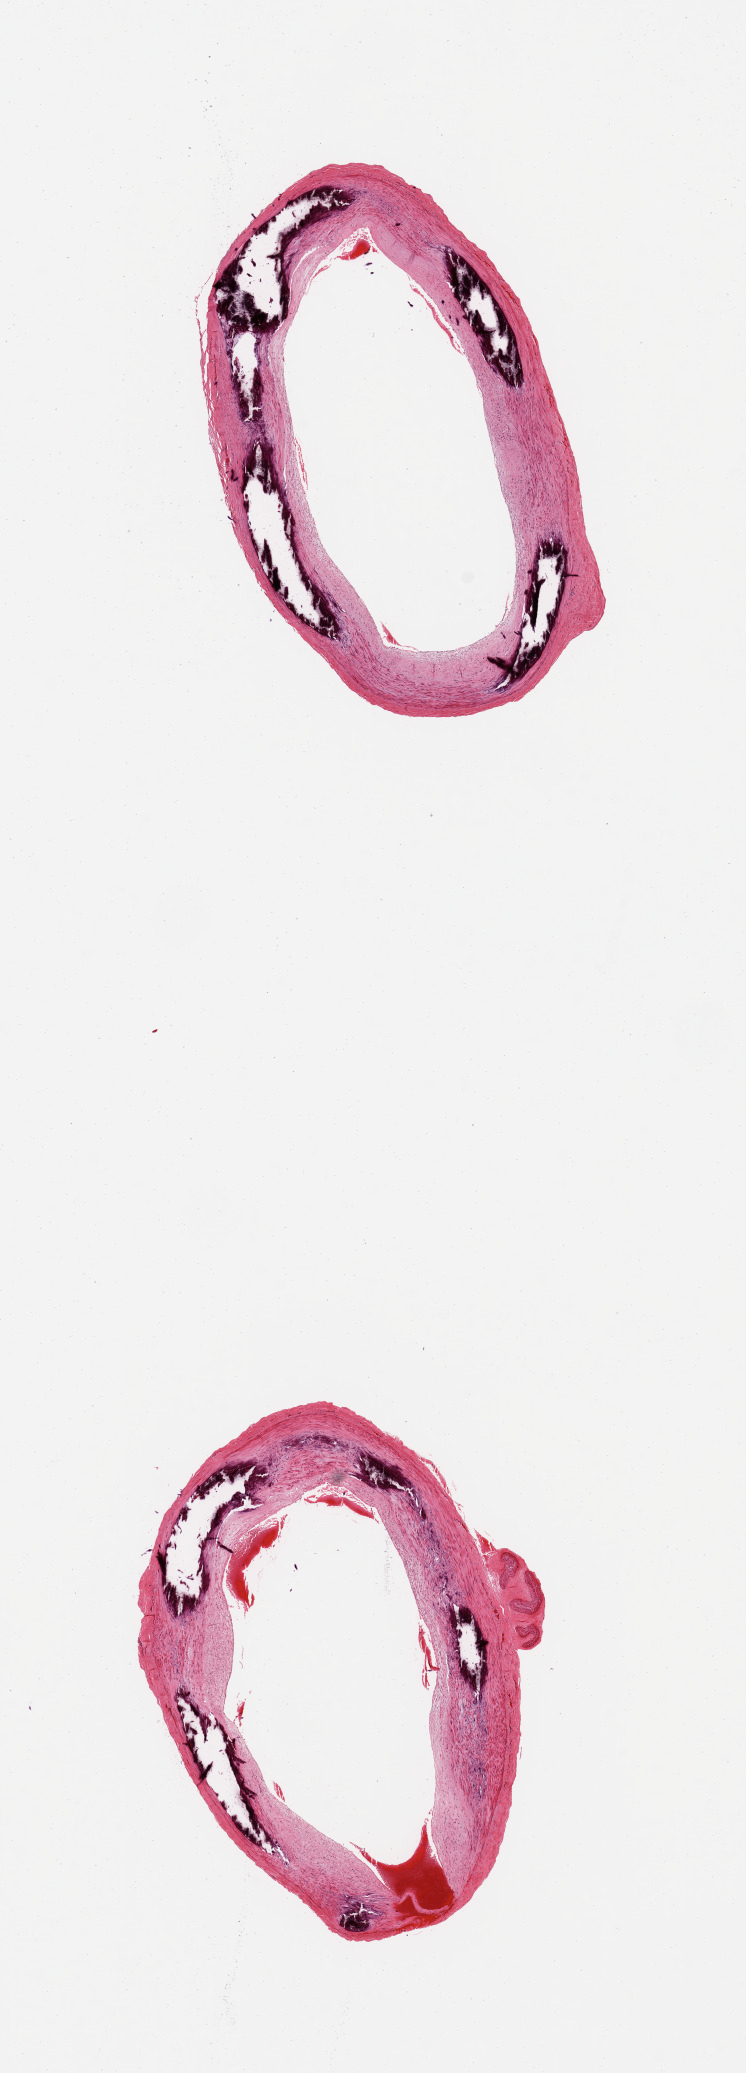
Digitized hematoxylin and eosin (H&E)-stained section, brightfield — whole scanned area (about 5.9 x 16.4 mm) shown as a low-resolution overview; PAXgene-fixed paraffin-embedded (PFPE) section; section of tibial artery (target tissue); donor tissue sample. Male donor.
Pathologist's review note for this sample: 2 pieces no adherent fat, minimal atherosis; prominent Monckeberg medial sclerosis.